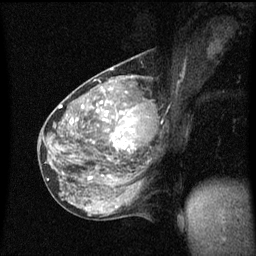
Breast MRI (dynamic contrast-enhanced), one sagittal slice. Slice 26 of 60 in the series (ordered by position). Dynamic contrast-enhanced series, image 2 of 3 at this slice position (ordered by acquisition). 1.5 T. TE 4.2 ms, TR 8.4 ms. 256 × 256 image matrix. Patient: female, 49 years.
Structures marked on this image (semi-automatic segmentation, software-assisted and operator-edited):
- analysis volume of interest (the breast-tissue region the enhancement analysis was run in; not a lesion): box from (x=103, y=90) to (x=157, y=151) px
- tumour enhancement mask (voxels above the 70 % enhancement threshold inside the analysis volume of interest): (x=103, y=102)–(x=135, y=151)